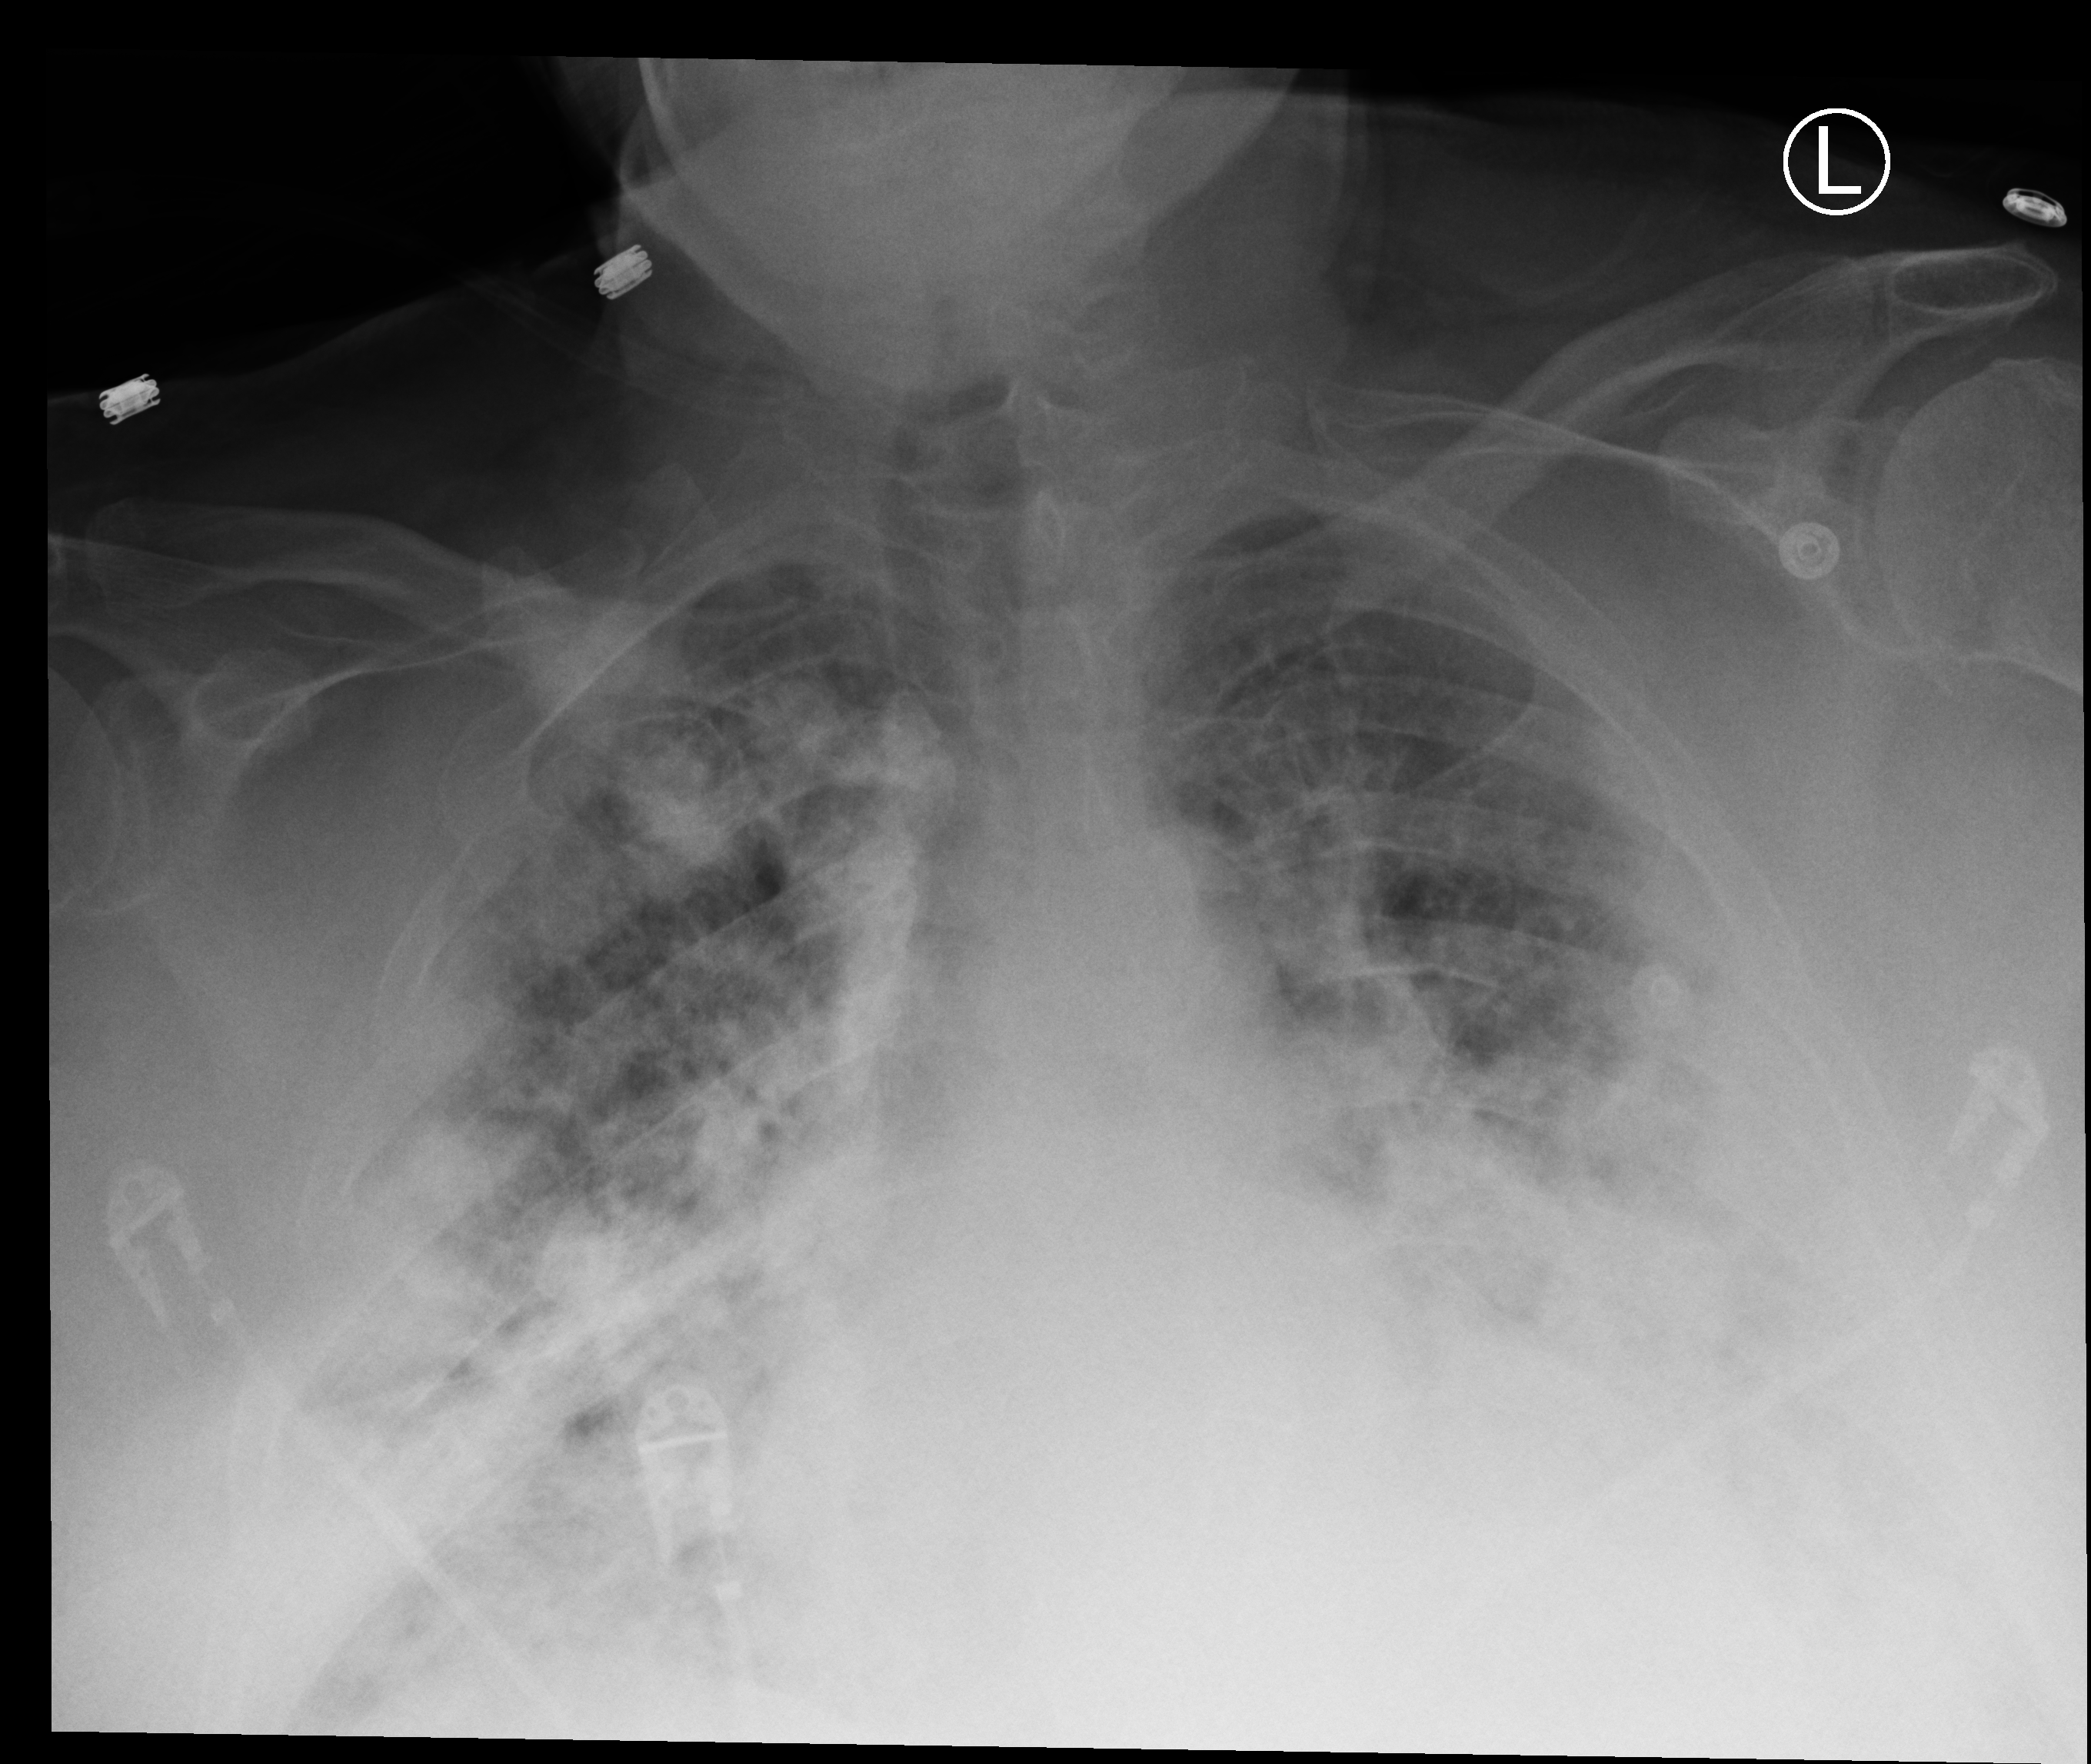
Chest X-ray (portable), anteroposterior (AP) projection. Patient hospitalised with COVID-19; male, aged 60–74 years.
Admission-level facts for this patient (not findings on this image; timing relative to this image not recorded): admitted to intensive care during this hospital stay: yes; mechanically ventilated during this hospital stay: yes; chronic kidney disease (admission record): yes.